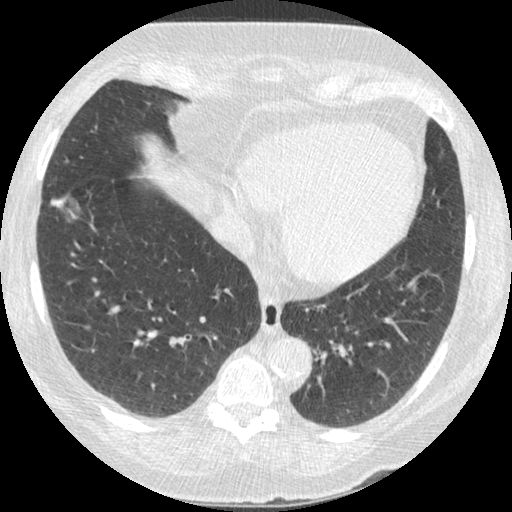
Low-dose screening chest CT, one axial slice; position 92 of 245 along the scan axis; reconstruction kernel STANDARD; 120 kVp; lung window (W 1500 / L -600 HU); 1.25 mm slice thickness; 512 × 512 image matrix, field of view 310 × 310 mm.
Annotated regions visible in this slice (outlined manually by an expert reader):
- lesion 1 (tumor, lower lobe of right lung): box from (x=50, y=195) to (x=79, y=220) px